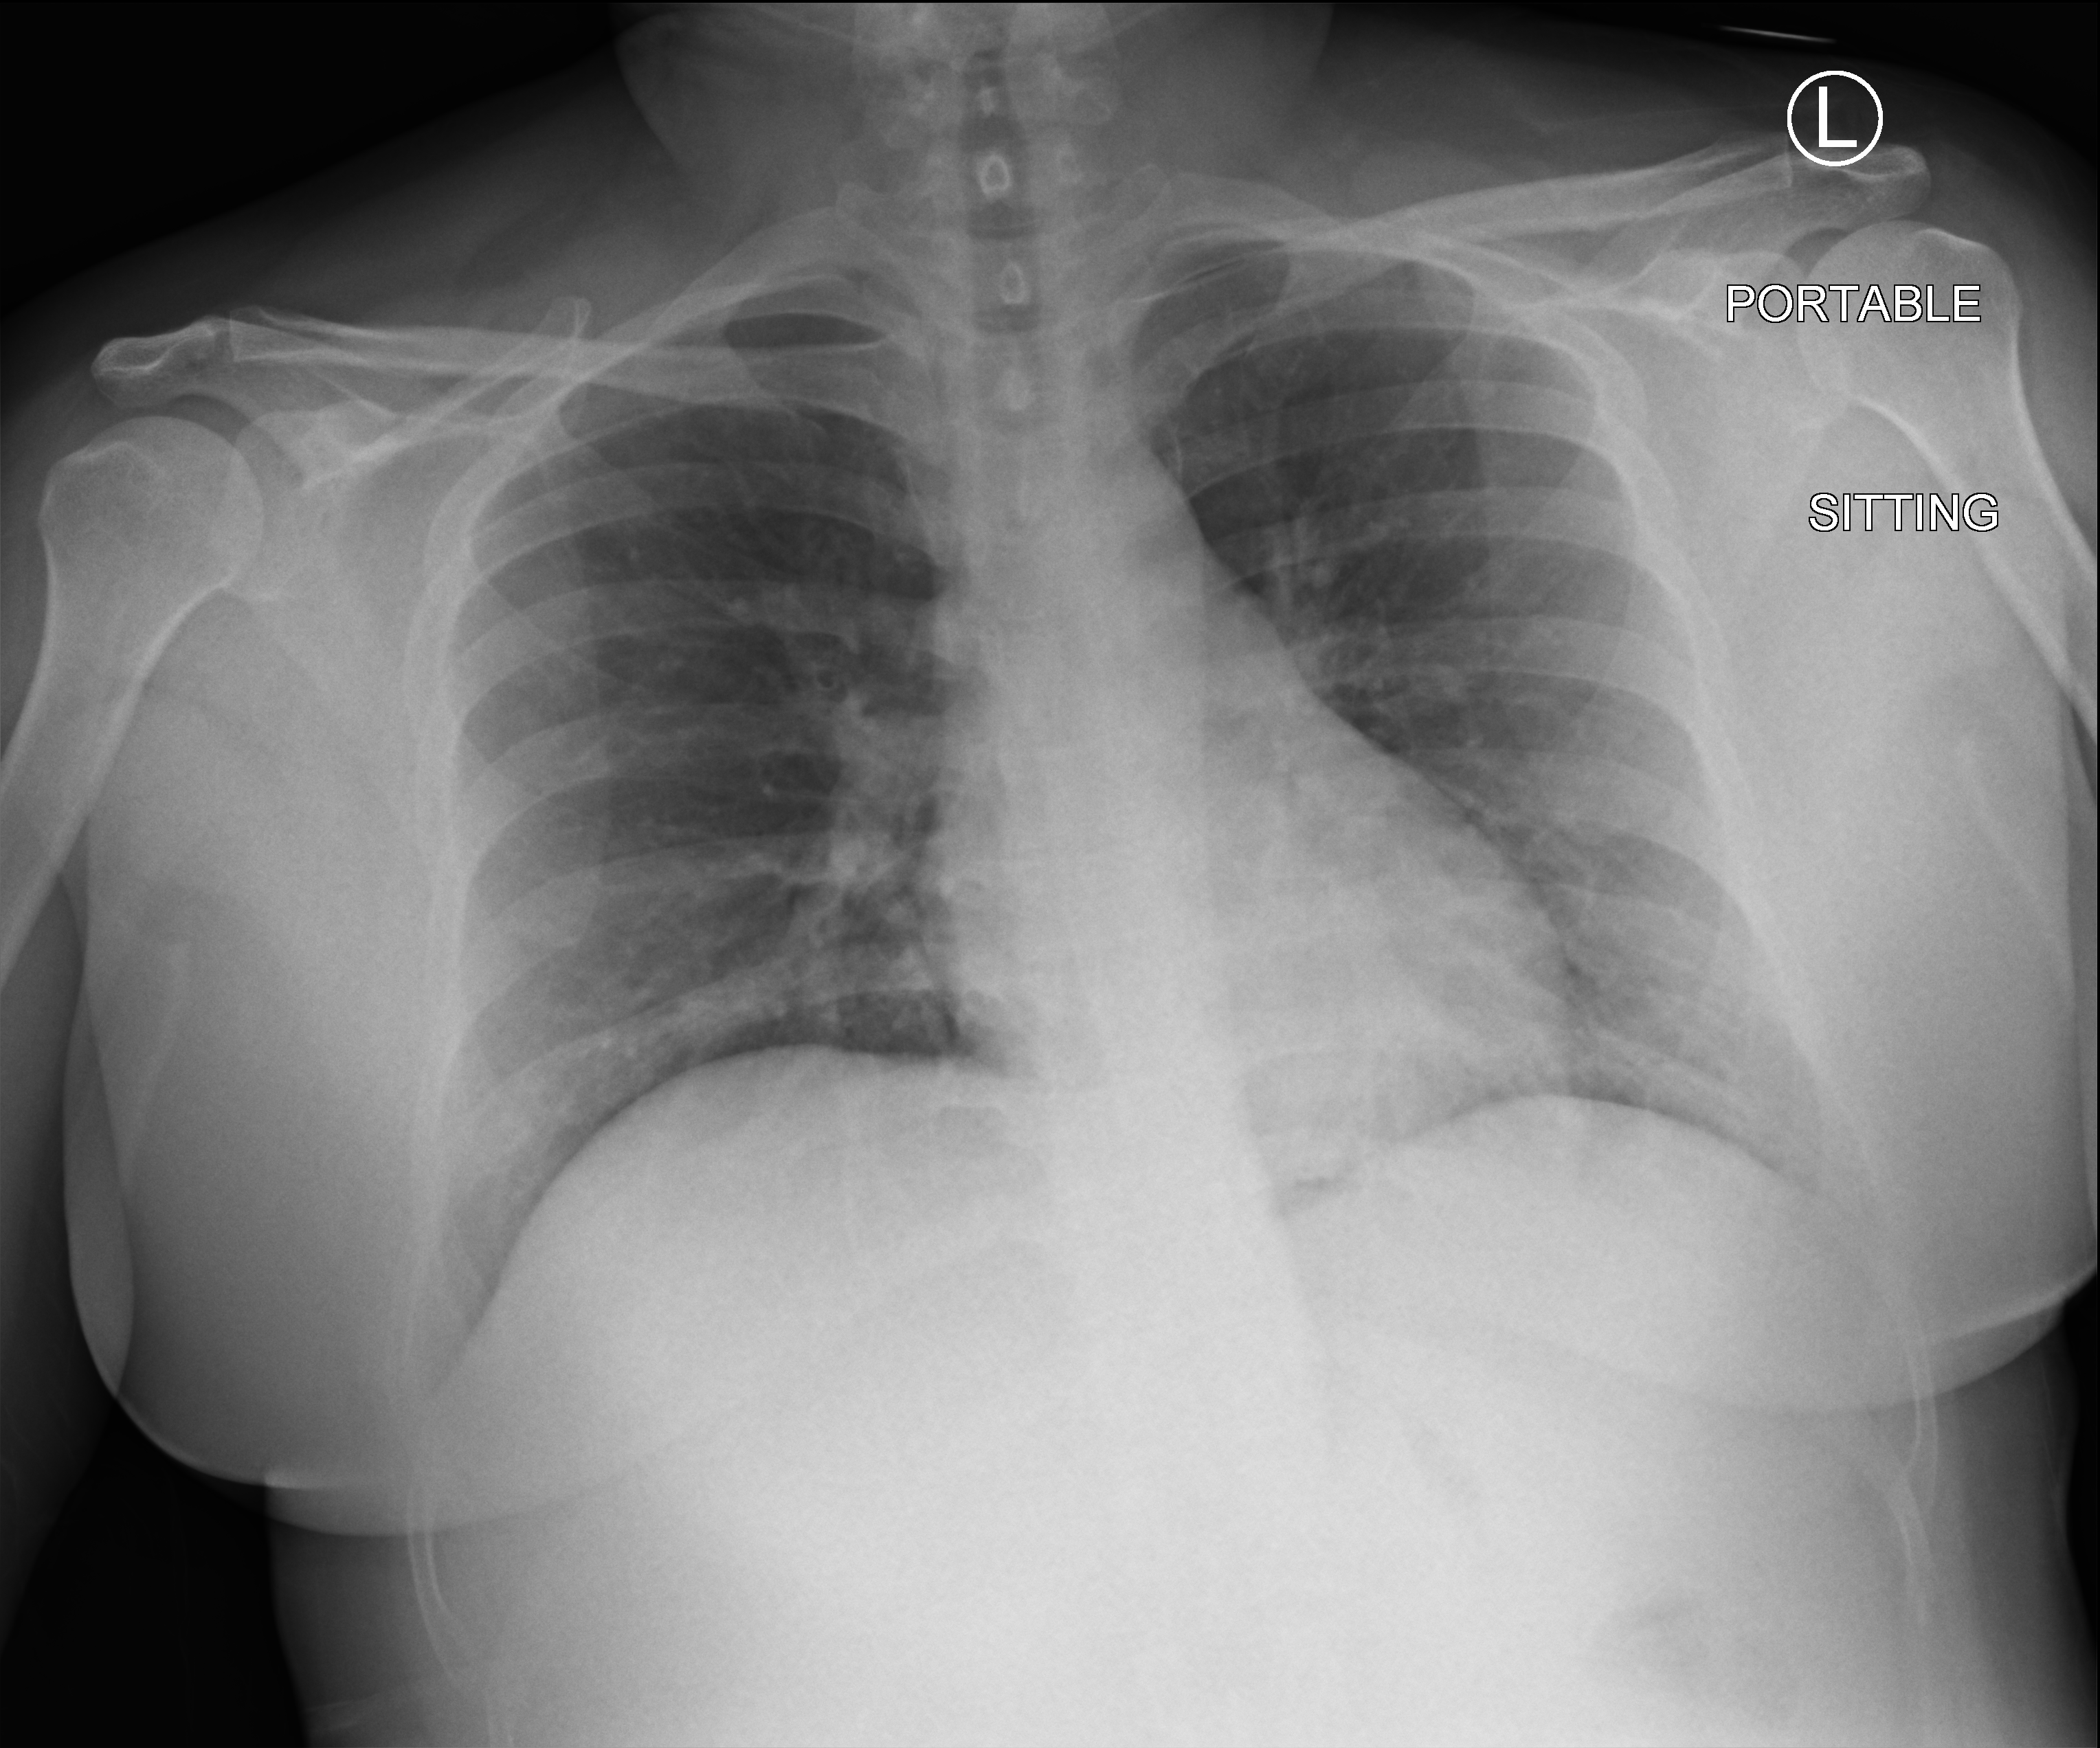
Chest X-ray (portable); anteroposterior (AP) projection. Female patient hospitalised with COVID-19, age 18–59 years.
Admission-level facts for this patient (not findings on this image; timing relative to this image not recorded): admitted to intensive care during this hospital stay: no.